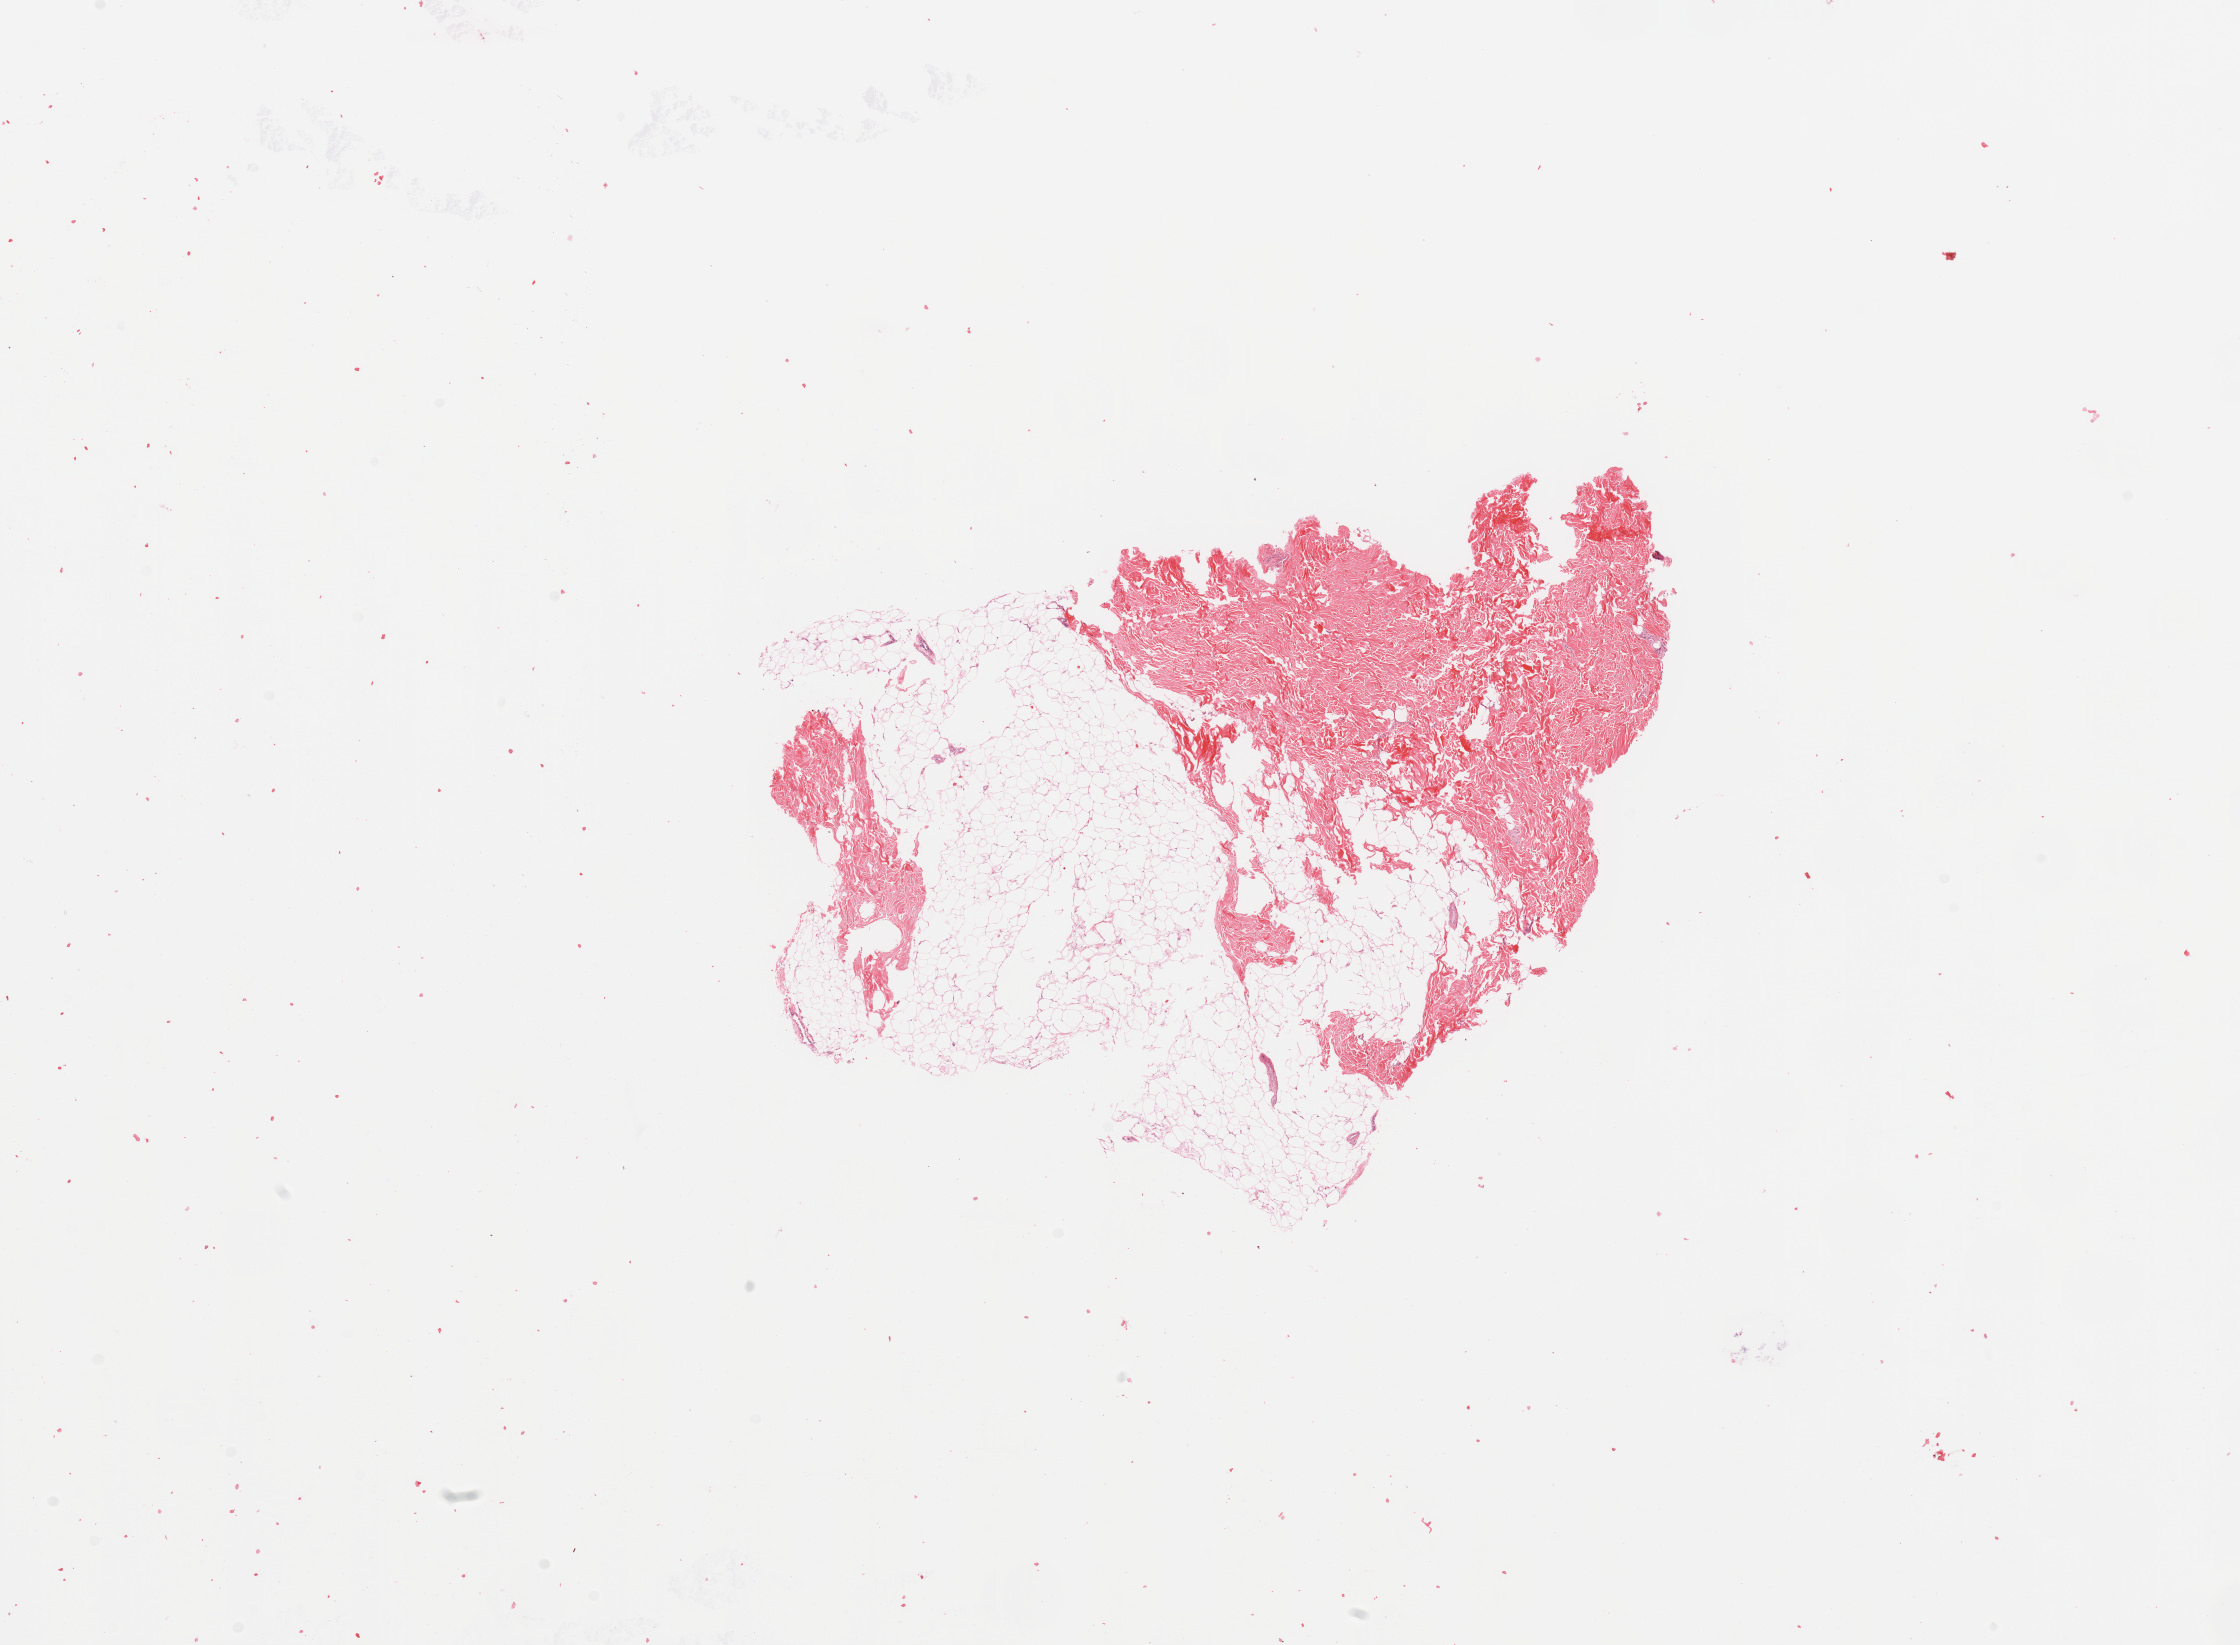
Whole-slide histology image, H&E — whole scanned area (about 17.7 x 13.0 mm, acquisition: 20x scan) shown as a low-resolution overview. Normal (non-tumour) tissue sample, sampled site: trunk. 34-year-old male patient.
This section: normal (non-tumour) tissue from the same patient. Patient diagnosis: Malignant melanoma, NOS.